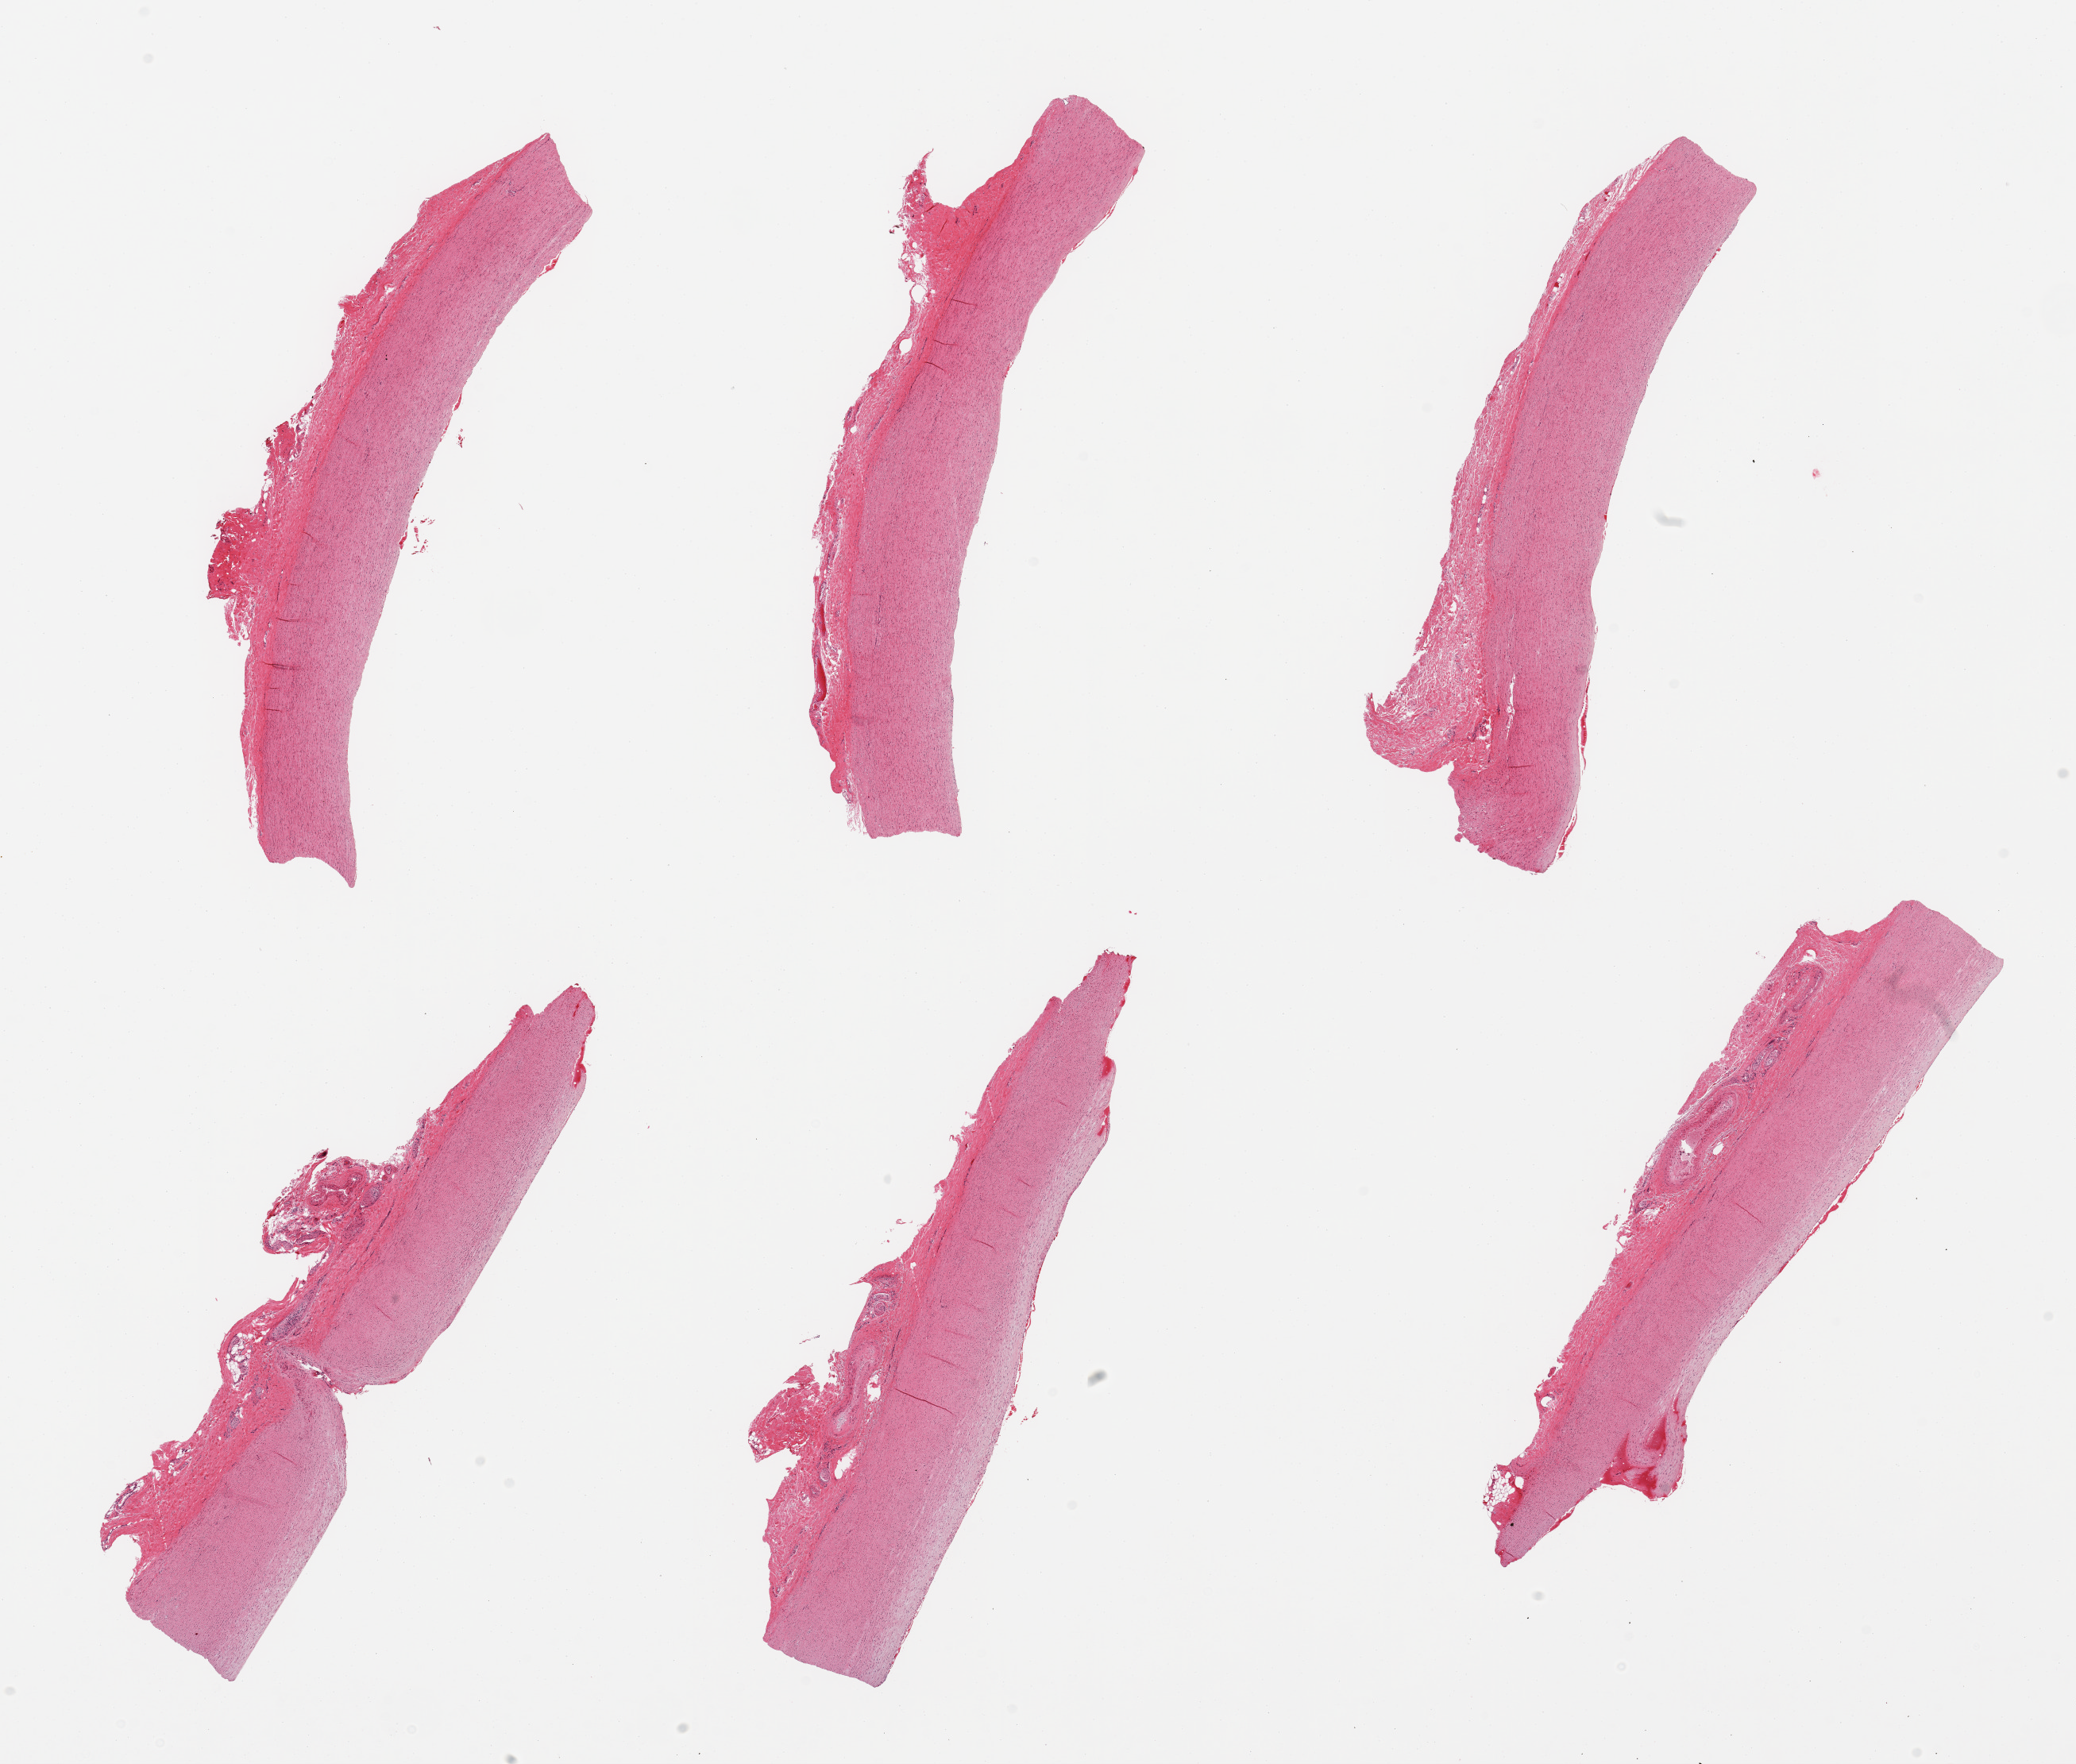
Digitized hematoxylin and eosin (H&E)-stained section, shown as a low-resolution overview of the whole scanned area (about 20.7 x 17.6 mm, acquisition: 20x scan), PAXgene-fixed, paraffin-embedded tissue, target tissue: aorta, tissue donor sample.
• review note (as recorded): 6 pieces, ~0.2mm layer of atherosis